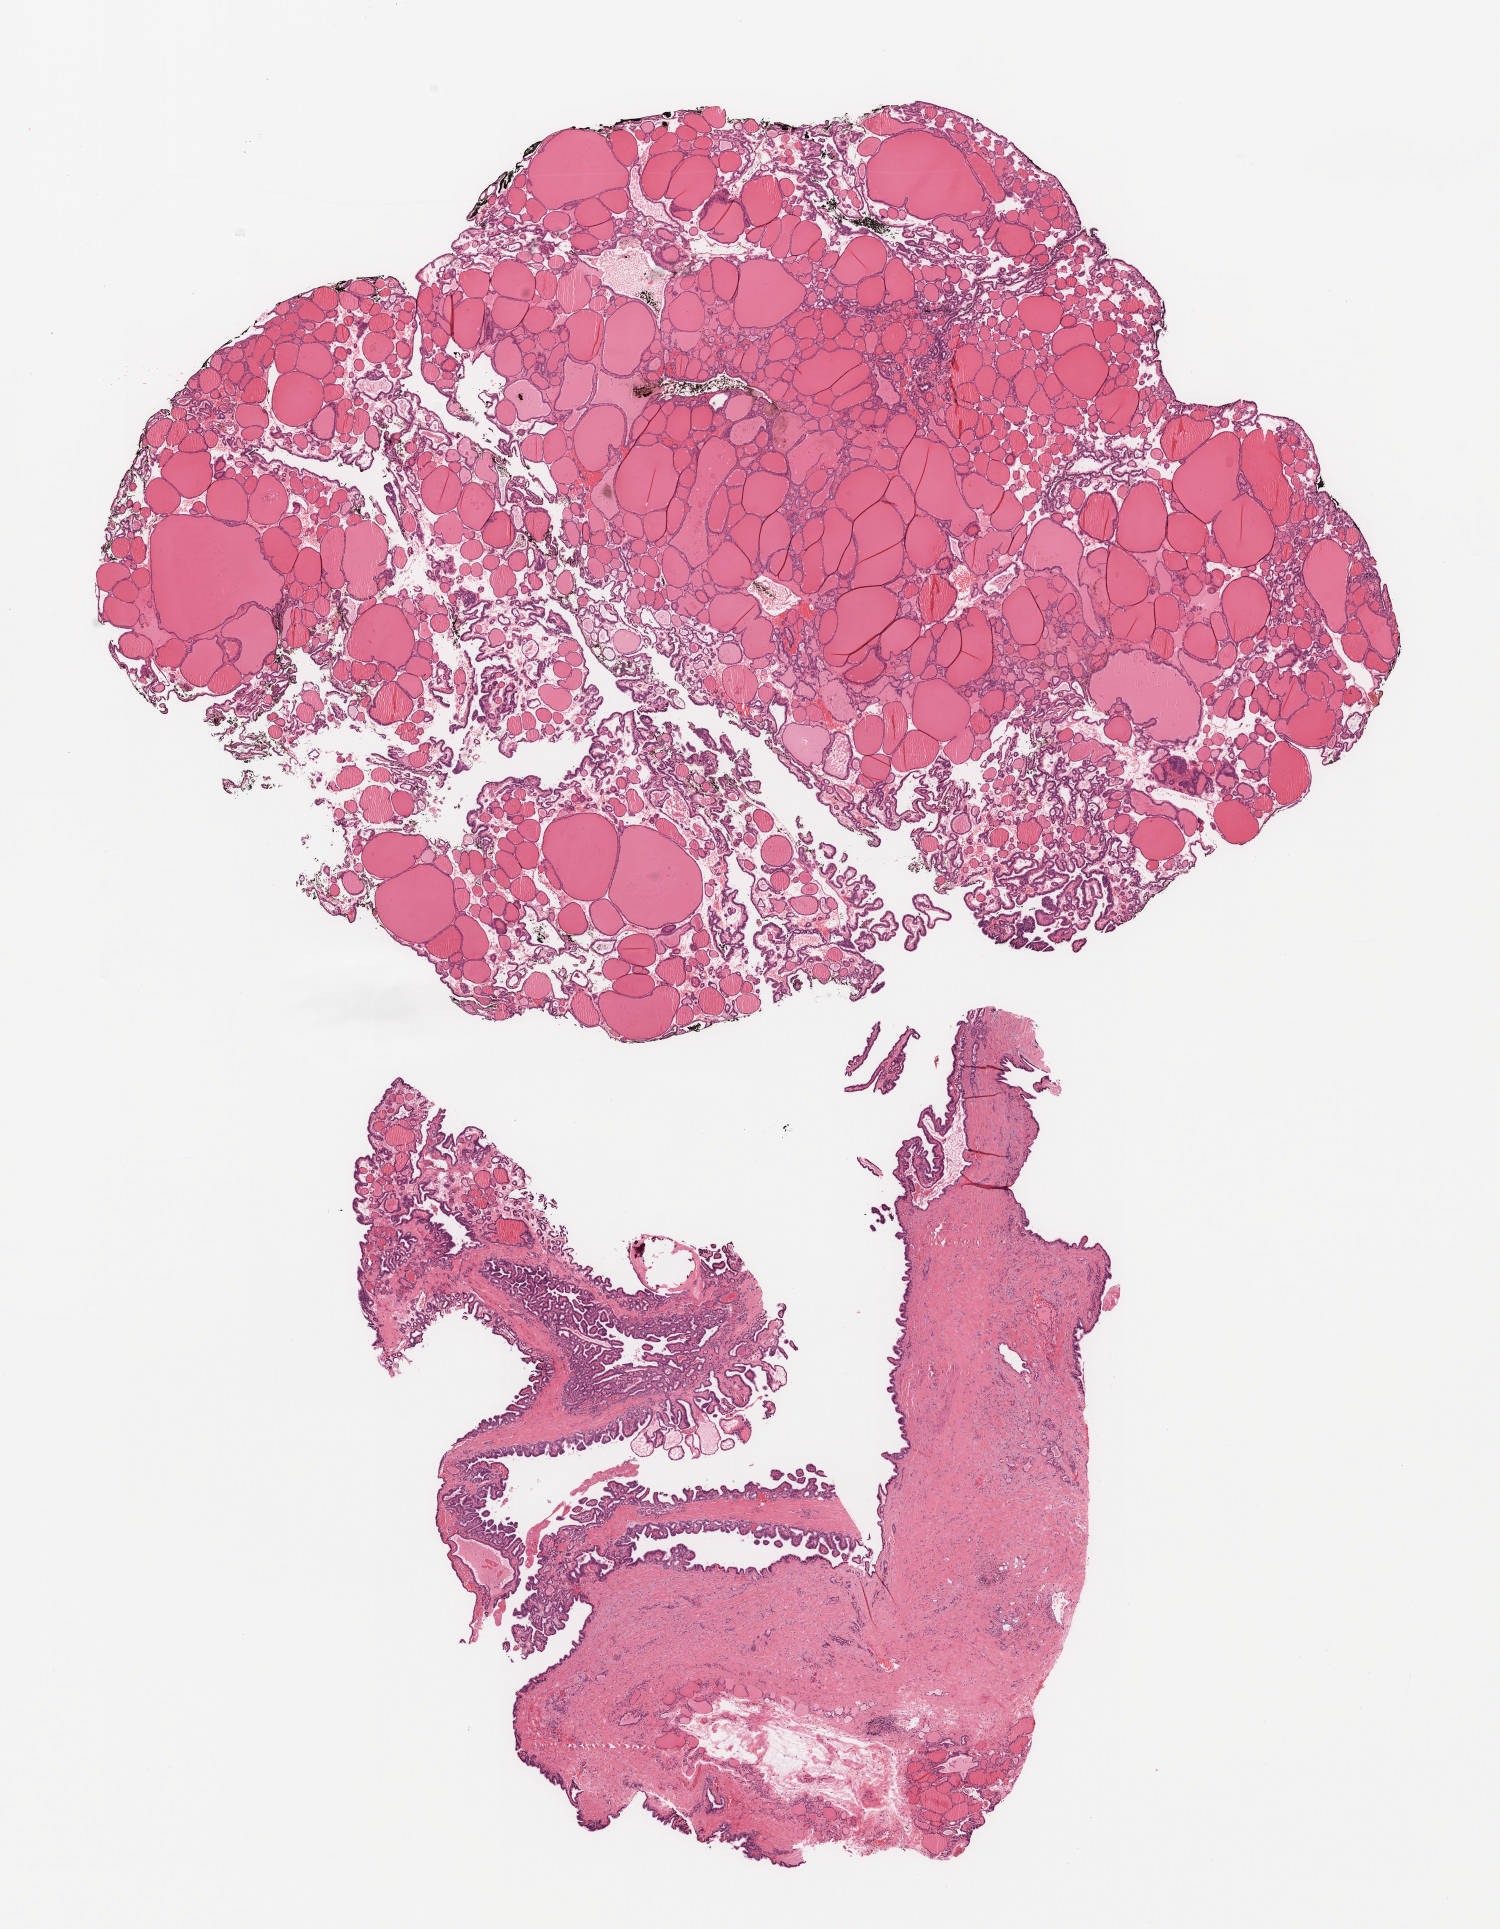
H&E whole-slide image, shown as a low-resolution overview of the whole scanned area (about 12.0 x 15.5 mm, from a 20x scan); formalin-fixed paraffin-embedded (FFPE) diagnostic section; thyroid, primary tumour sample. Patient: female, age at initial diagnosis 46 years.
Pathologic diagnosis: Papillary adenocarcinoma, NOS (thyroid gland). AJCC pathologic stage: III (7th edition). Laterality: right.